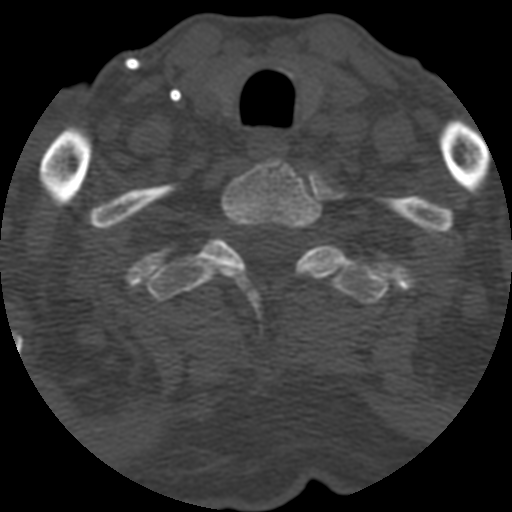
CT including the spine, one axial slice; position 512 of 708 along the scan axis; reconstruction kernel STANDARD; one of 3 acquisitions stored at this slice position; bone window (W 1800 / L 400 HU); 1.25 mm slice thickness; 512 × 512 image matrix, field of view 160 × 160 mm. Patient age 55 years. Case-level facts recorded for this patient, not image findings: primary cancer: colon; vertebrae with lytic lesions (as recorded): T12, L1, L5.
Outlined on this slice (semi-automatically segmented with operator editing):
- T1 vertebra: bounding box <206,161,342,300> (left, top, right, bottom; pixels)
- T2 vertebra: <148,238,387,303>